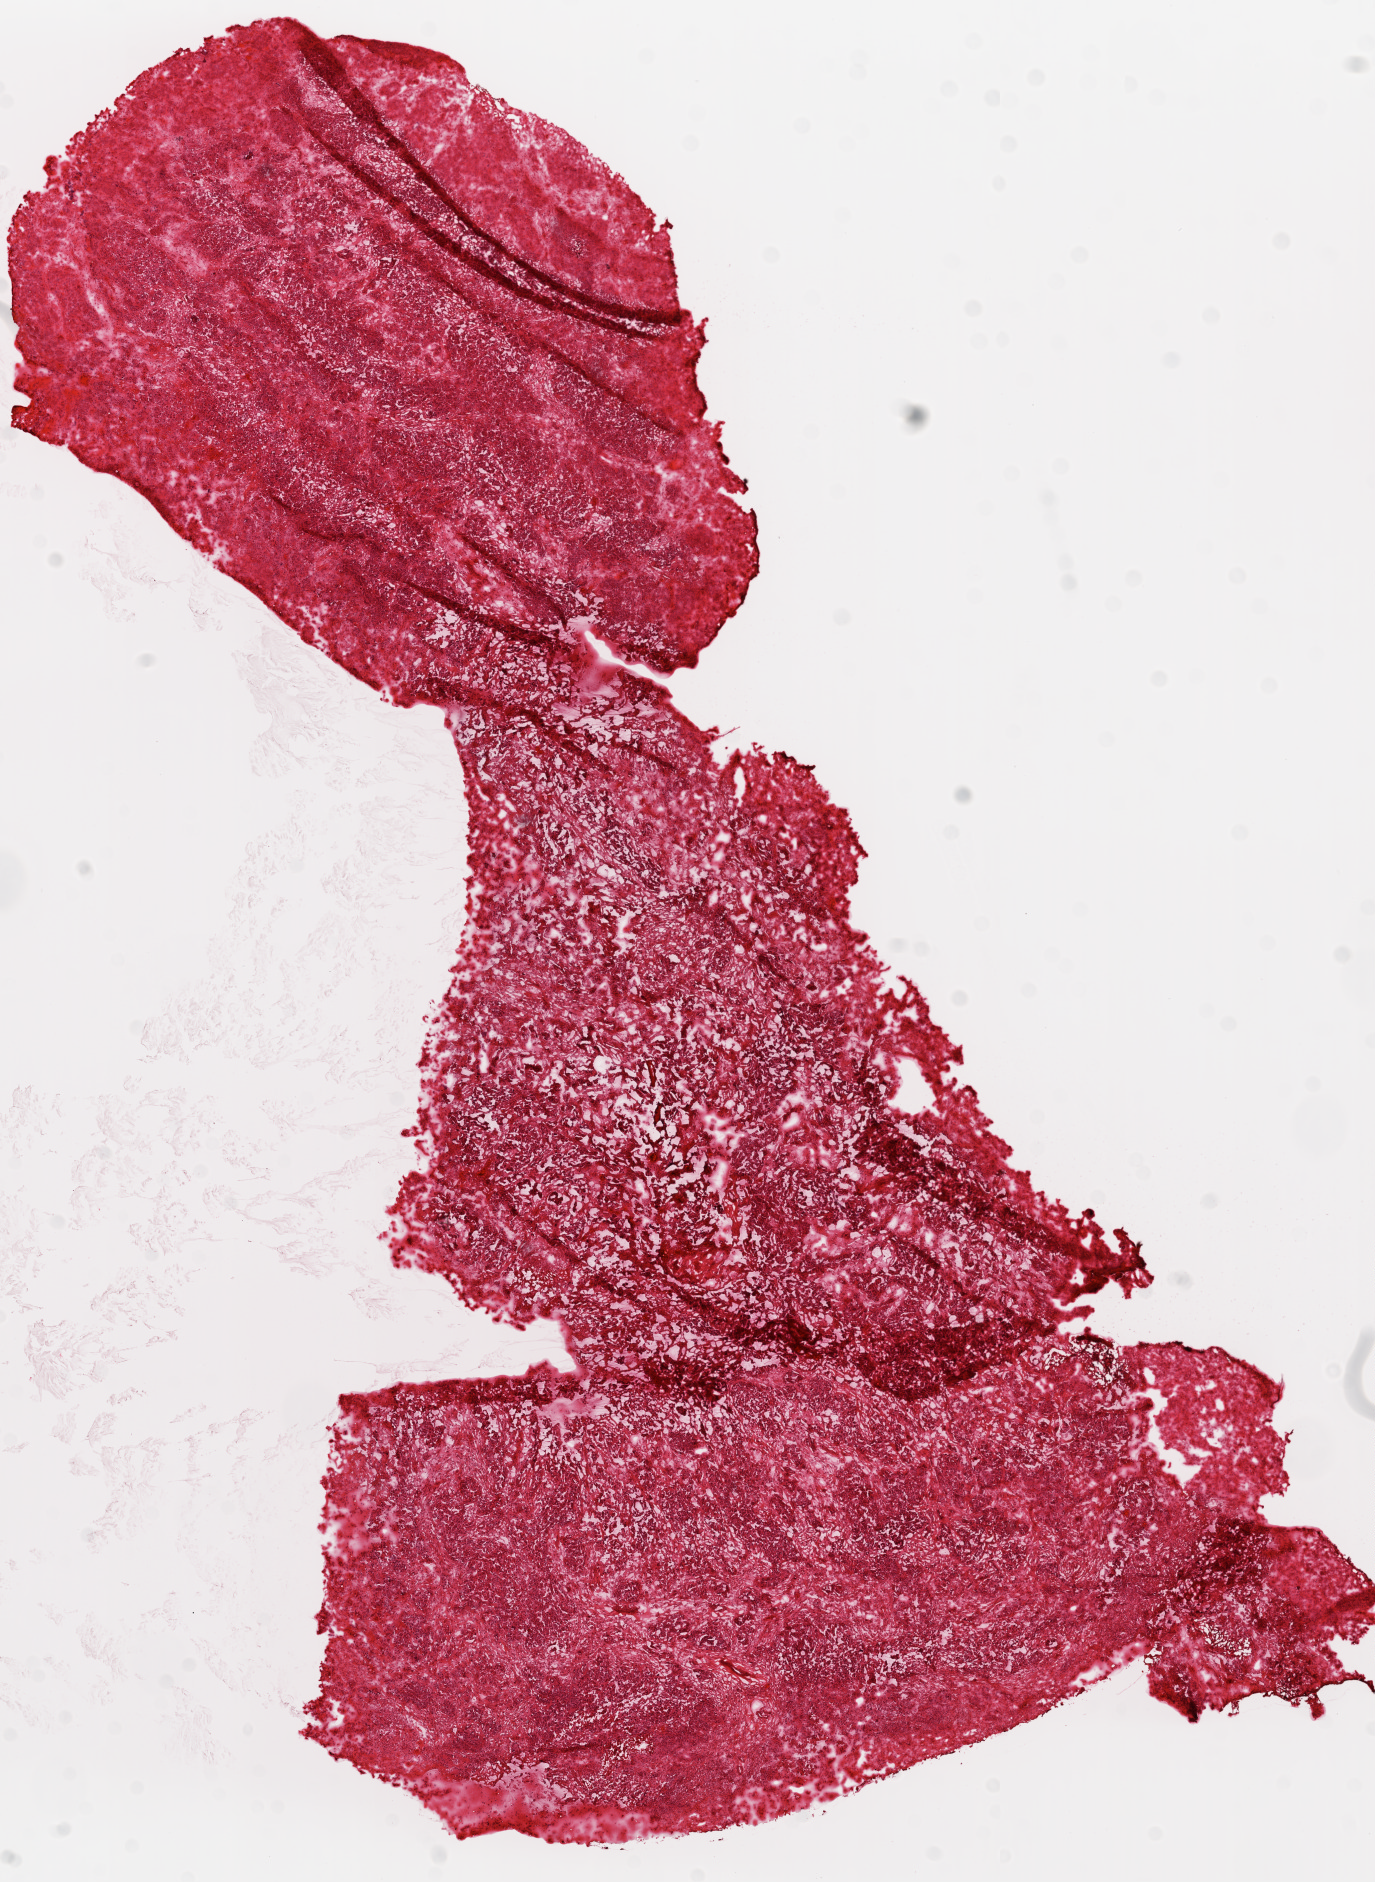
Digitized H&E tissue section (whole slide), low-resolution overview of the scanned area, about 11.0 x 15.1 mm (acquisition: 20x scan). Frozen section. Ovary, primary tumour sample. Female patient; age at initial diagnosis 57 years. Histologic grade: G3 (poorly differentiated). Slide review estimates, as recorded: tumour cells 90%, tumour nuclei 90%, normal cells 0%, stromal cells 10%, necrosis 0%.
Laterality: right. FIGO stage: IIIC. Diagnosis: Serous cystadenocarcinoma, NOS.